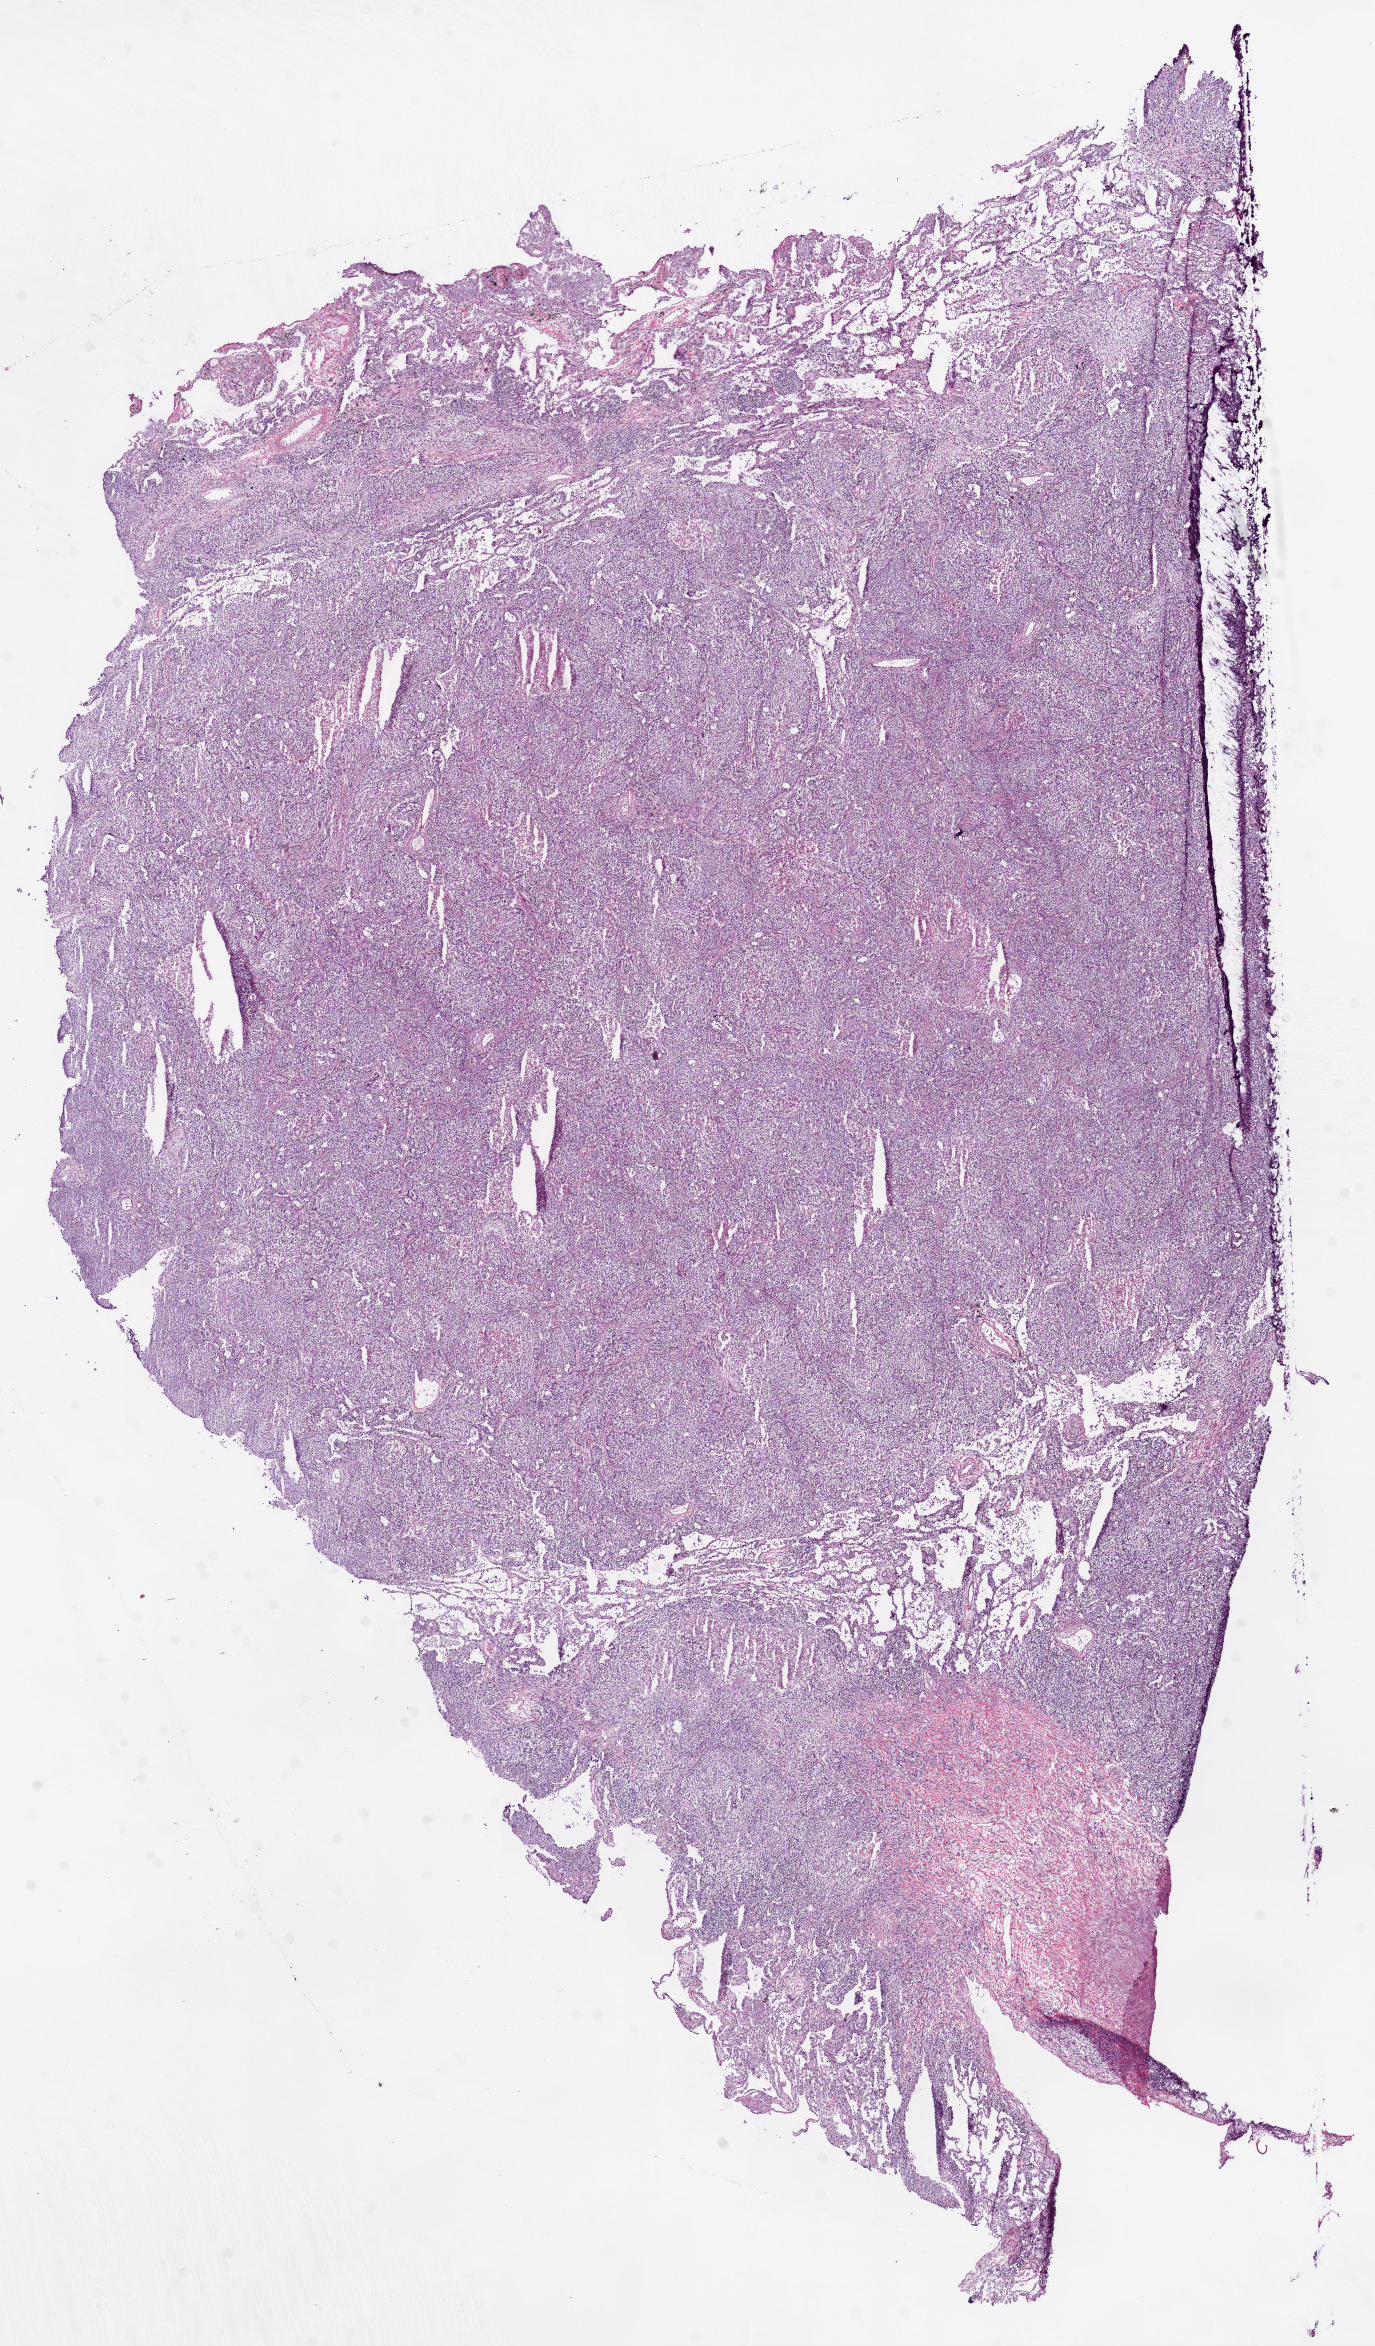
Whole-slide histology image, H&E-stained, low-resolution overview of the scanned area, about 11.0 x 18.8 mm (from a 20x scan); frozen section from the top of the tissue portion; sample: primary tumour, lung. Female patient; age at initial diagnosis 73 years. Slide review estimates, as recorded: tumour cells 95%, tumour nuclei 80%, normal cells 0%, stromal cells 0%, necrosis 5%. Inflammatory infiltration, as recorded: lymphocyte infiltration 10%, monocyte infiltration 1%, neutrophil infiltration 2%.
* pathologic diagnosis: Squamous cell carcinoma, NOS (upper lobe, lung)
* AJCC pathologic stage: IIIA